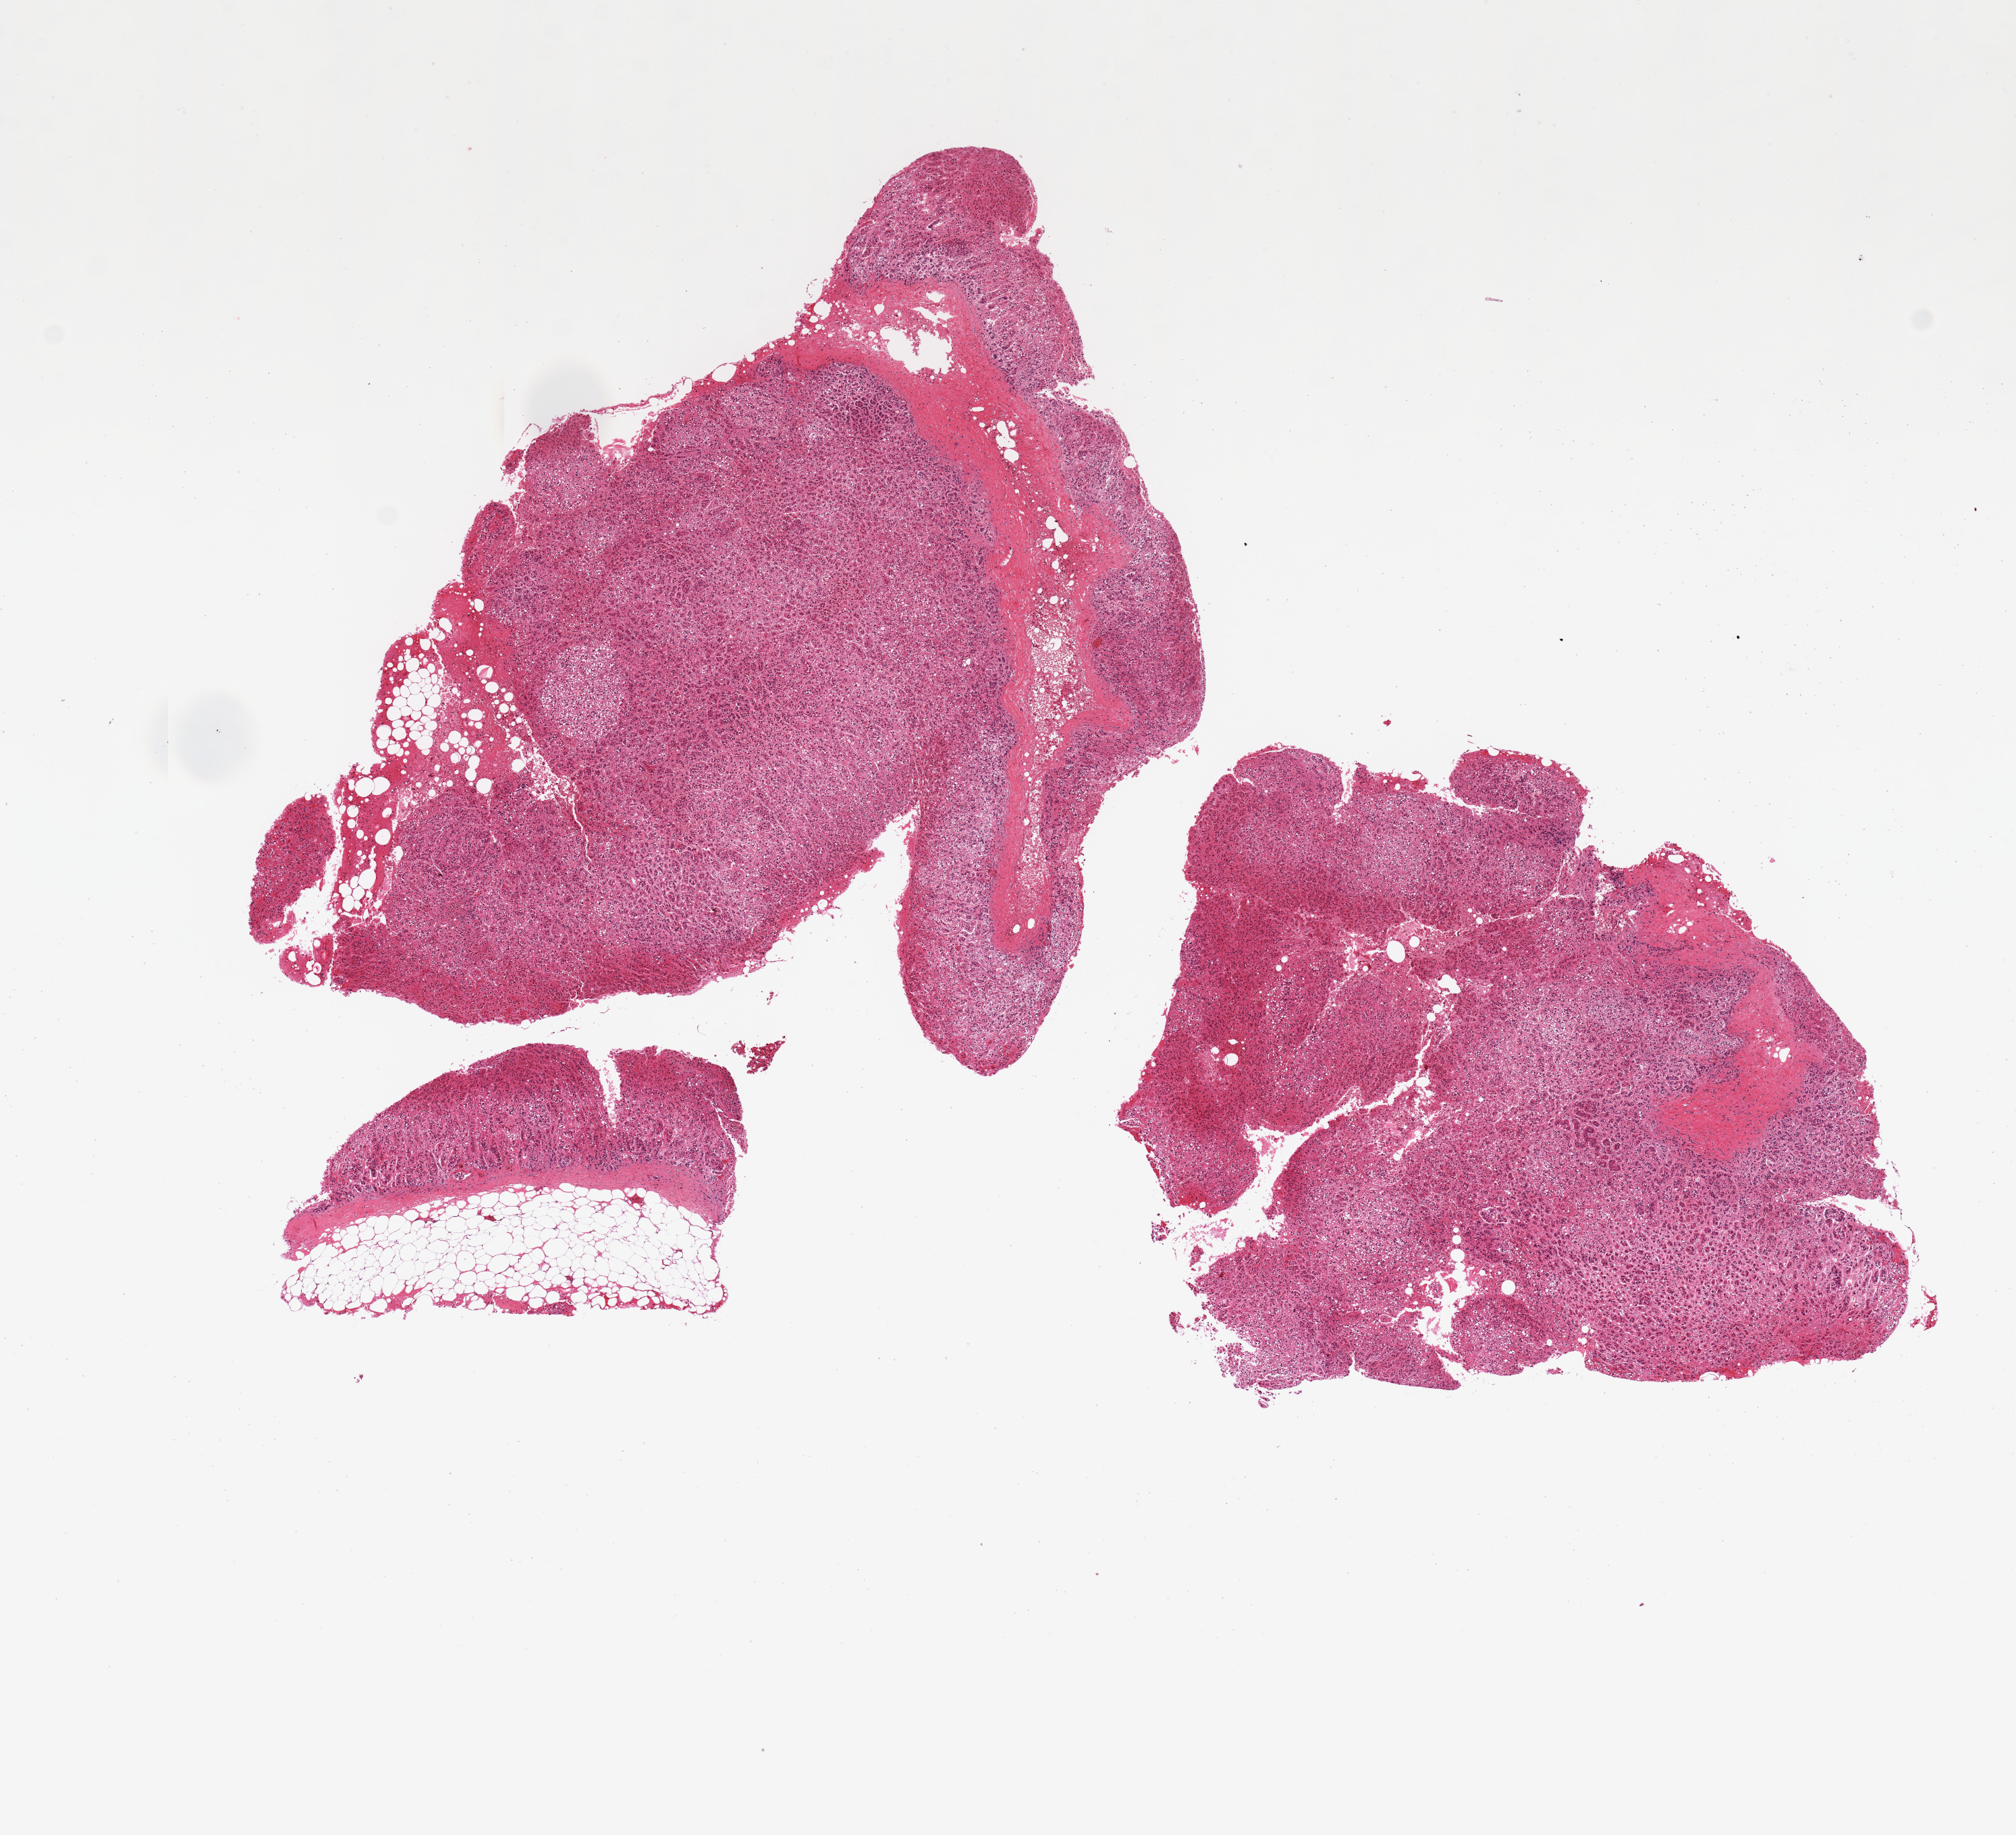
Digitized H&E-stained section, brightfield — low-resolution overview of the scanned area, about 11.8 x 10.8 mm. PAXgene-fixed, paraffin-embedded tissue. Section of adrenal gland (target tissue). Tissue donor sample. Donor sex: male.
- pathologist's review note for this sample: 3 pieces, small amount of untrimmed fat